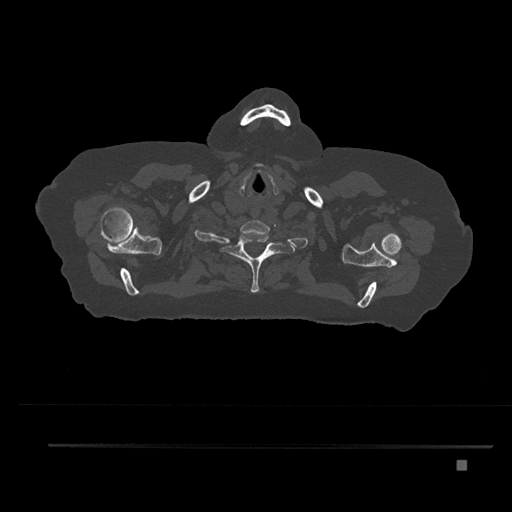
CT including the spine, one axial slice. Position 703 of 797 along the scan axis. Reconstruction kernel Br40s/3. 120 kVp. Bone window (W 1800 / L 400 HU). 512 × 512 image matrix. Female patient, age 76 years. Case-level facts recorded for this patient, not image findings: primary cancer: lung; vertebrae with lytic lesions (as recorded): T11, L3.
Structures marked on this image (semi-automatically segmented with operator editing):
- T1 vertebra: box from (x=223, y=233) to (x=283, y=293) px